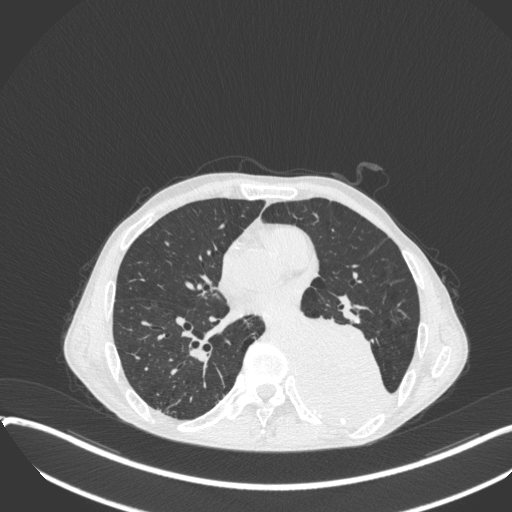
Chest CT, one axial slice; slice 167 of 400 in the series (ordered by position); lung window (W 1500 / L -600 HU); 512 × 512 image matrix, field of view 400 × 400 mm. Patient: male, 57 years. From the clinical record (not read from this slice): clinical TNM (as recorded): T4 N0 M0.
Annotated regions visible in this slice (bounding box drawn by a radiologist):
- lung tumour (recorded histology: squamous cell carcinoma): box from (x=299, y=311) to (x=395, y=428) px